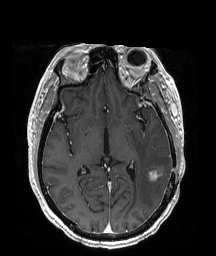
Brain MRI from a brain-tumour surgery series, one axial slice; slice 100 of 192 in the series (ordered by position); T1-weighted post-contrast; 1 mm slice thickness; 216 × 256 image matrix, field of view 211 × 250 mm. From the clinical record (not read from this slice): histopathology: Glioblastoma; WHO grade: 4; IDH mutation: no; tumour location: Left Temporoparietal.
Structures marked on this image (outlined manually by an expert reader):
- tumour: bounding box (x1, y1, x2, y2) in pixels: (151, 168, 163, 178)